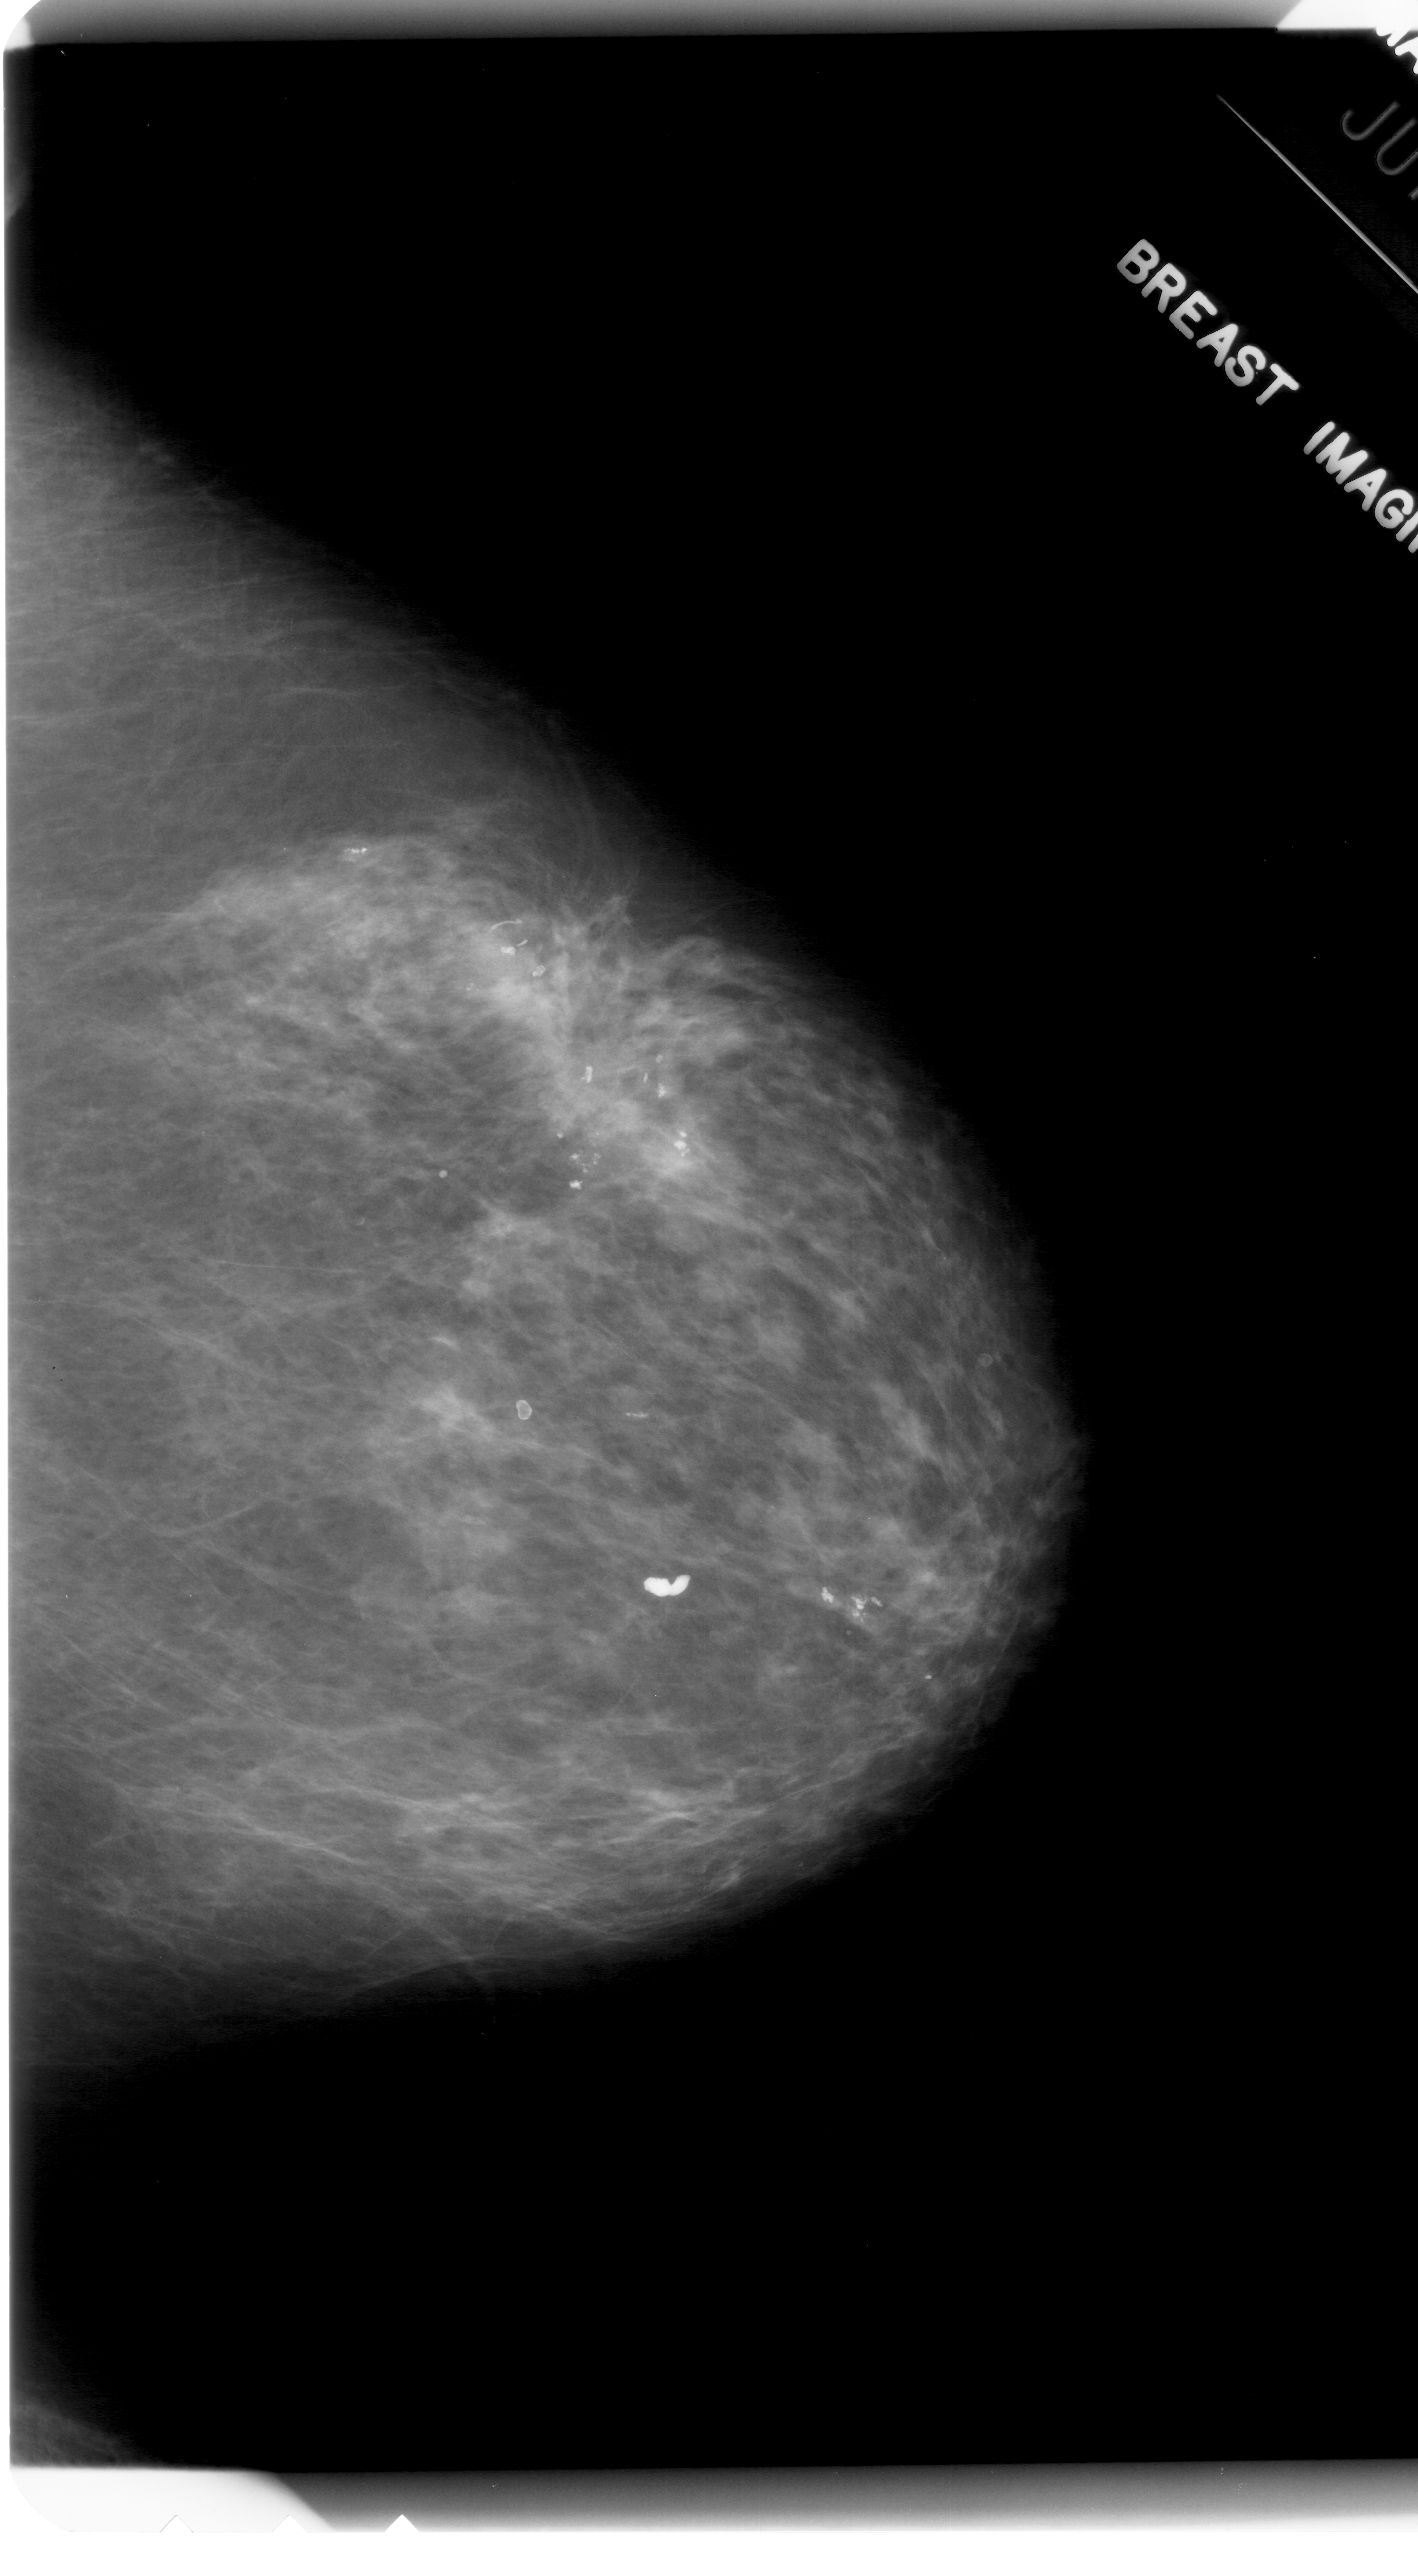
Scanned film-screen mammogram; right breast; craniocaudal (CC) view; BI-RADS breast density category 3 (scale 1–4).
Marked findings (only marked abnormalities are described; nothing is implied about the rest of the image): Finding 1 of 3: calcifications, morphology dystrophic, distribution clustered; BI-RADS assessment category 3; subtlety rating 4 on a 1 (subtle) to 5 (obvious) scale; pathology result (as recorded, not read from the image): benign. Finding 2 of 3: calcifications, morphology dystrophic, distribution clustered; BI-RADS assessment category 3; subtlety rating 4 on a 1 (subtle) to 5 (obvious) scale; pathology result (as recorded, not read from the image): benign. Finding 3 of 3: calcifications, morphology dystrophic, distribution clustered; BI-RADS assessment category 3; pathology (as recorded): benign.